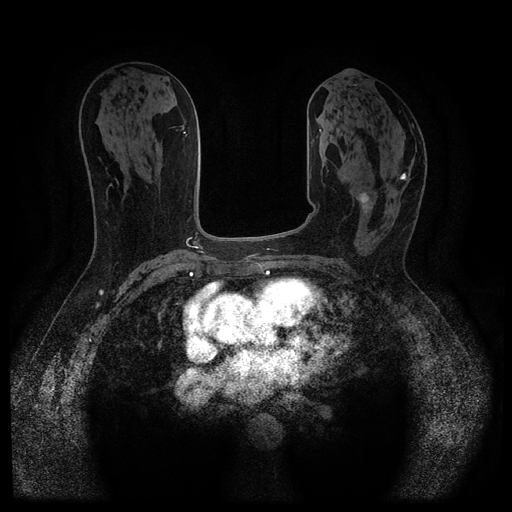
Breast MRI (dynamic contrast-enhanced, multi-phase), one axial slice. Slice 52 of 116 in the series (ordered by position). Dynamic contrast-enhanced series, time point 2 of 5 at this slice position (early post-contrast). 1.5 T. TE 2.6 ms, TR 5.4 ms. 2 mm slice thickness. 512 × 512 image matrix. Female patient, age 64 years.
Outlined on this slice (semi-automatic segmentation, software-assisted and operator-edited):
- breast lesion (labelled 'tumour' in the annotation; benign lesions carry a separate 'benign' label): bounding box <359,192,373,213> (left, top, right, bottom; pixels)